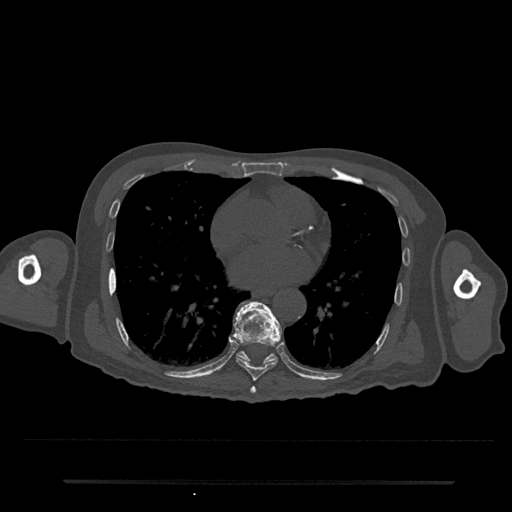
CT including the spine, one axial slice. Reconstruction kernel Br40s/3. 120 kVp. Bone window (W 1800 / L 400 HU). 0.5 mm slice thickness. 512 × 512 image matrix, field of view 427 × 427 mm. Patient: male, 74 years. Case-level facts recorded for this patient, not image findings: primary cancer: prostate.
Structures marked on this image (semi-automatically segmented with operator editing):
- T7 vertebra: bounding box (x1, y1, x2, y2) in pixels: (250, 386, 256, 394)
- T8 vertebra: (233, 301, 282, 381)
- T9 vertebra: (236, 308, 277, 364)